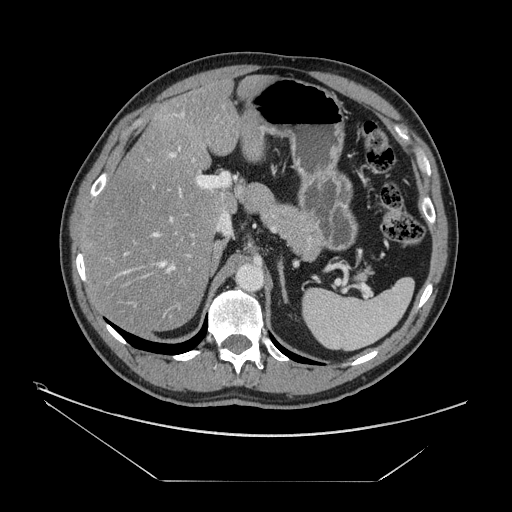
Contrast-enhanced abdominal CT, one axial slice. Position 94 of 161 along the scan axis. Reconstruction kernel STANDARD. 120 kVp. Intravenous contrast given. Soft-tissue window (W 400 / L 40 HU). 2.5 mm slice thickness. 512 × 512 image matrix, field of view 440 × 440 mm. Male patient, age 65 years. From the clinical record (not read from this slice): diagnosis: colorectal cancer liver metastases, imaged before liver resection; multiple liver metastases: yes; largest metastasis: 4.2 cm; disease in both lobes: yes.
Annotated regions visible in this slice (expert manual segmentation):
- hepatic veins: bounding box <118,186,182,275> (left, top, right, bottom; pixels)
- liver: <86,78,272,330>
- planned liver remnant (the part of the liver to remain after resection): <85,77,272,330>
- portal vein (with intrahepatic branches): <122,148,229,318>